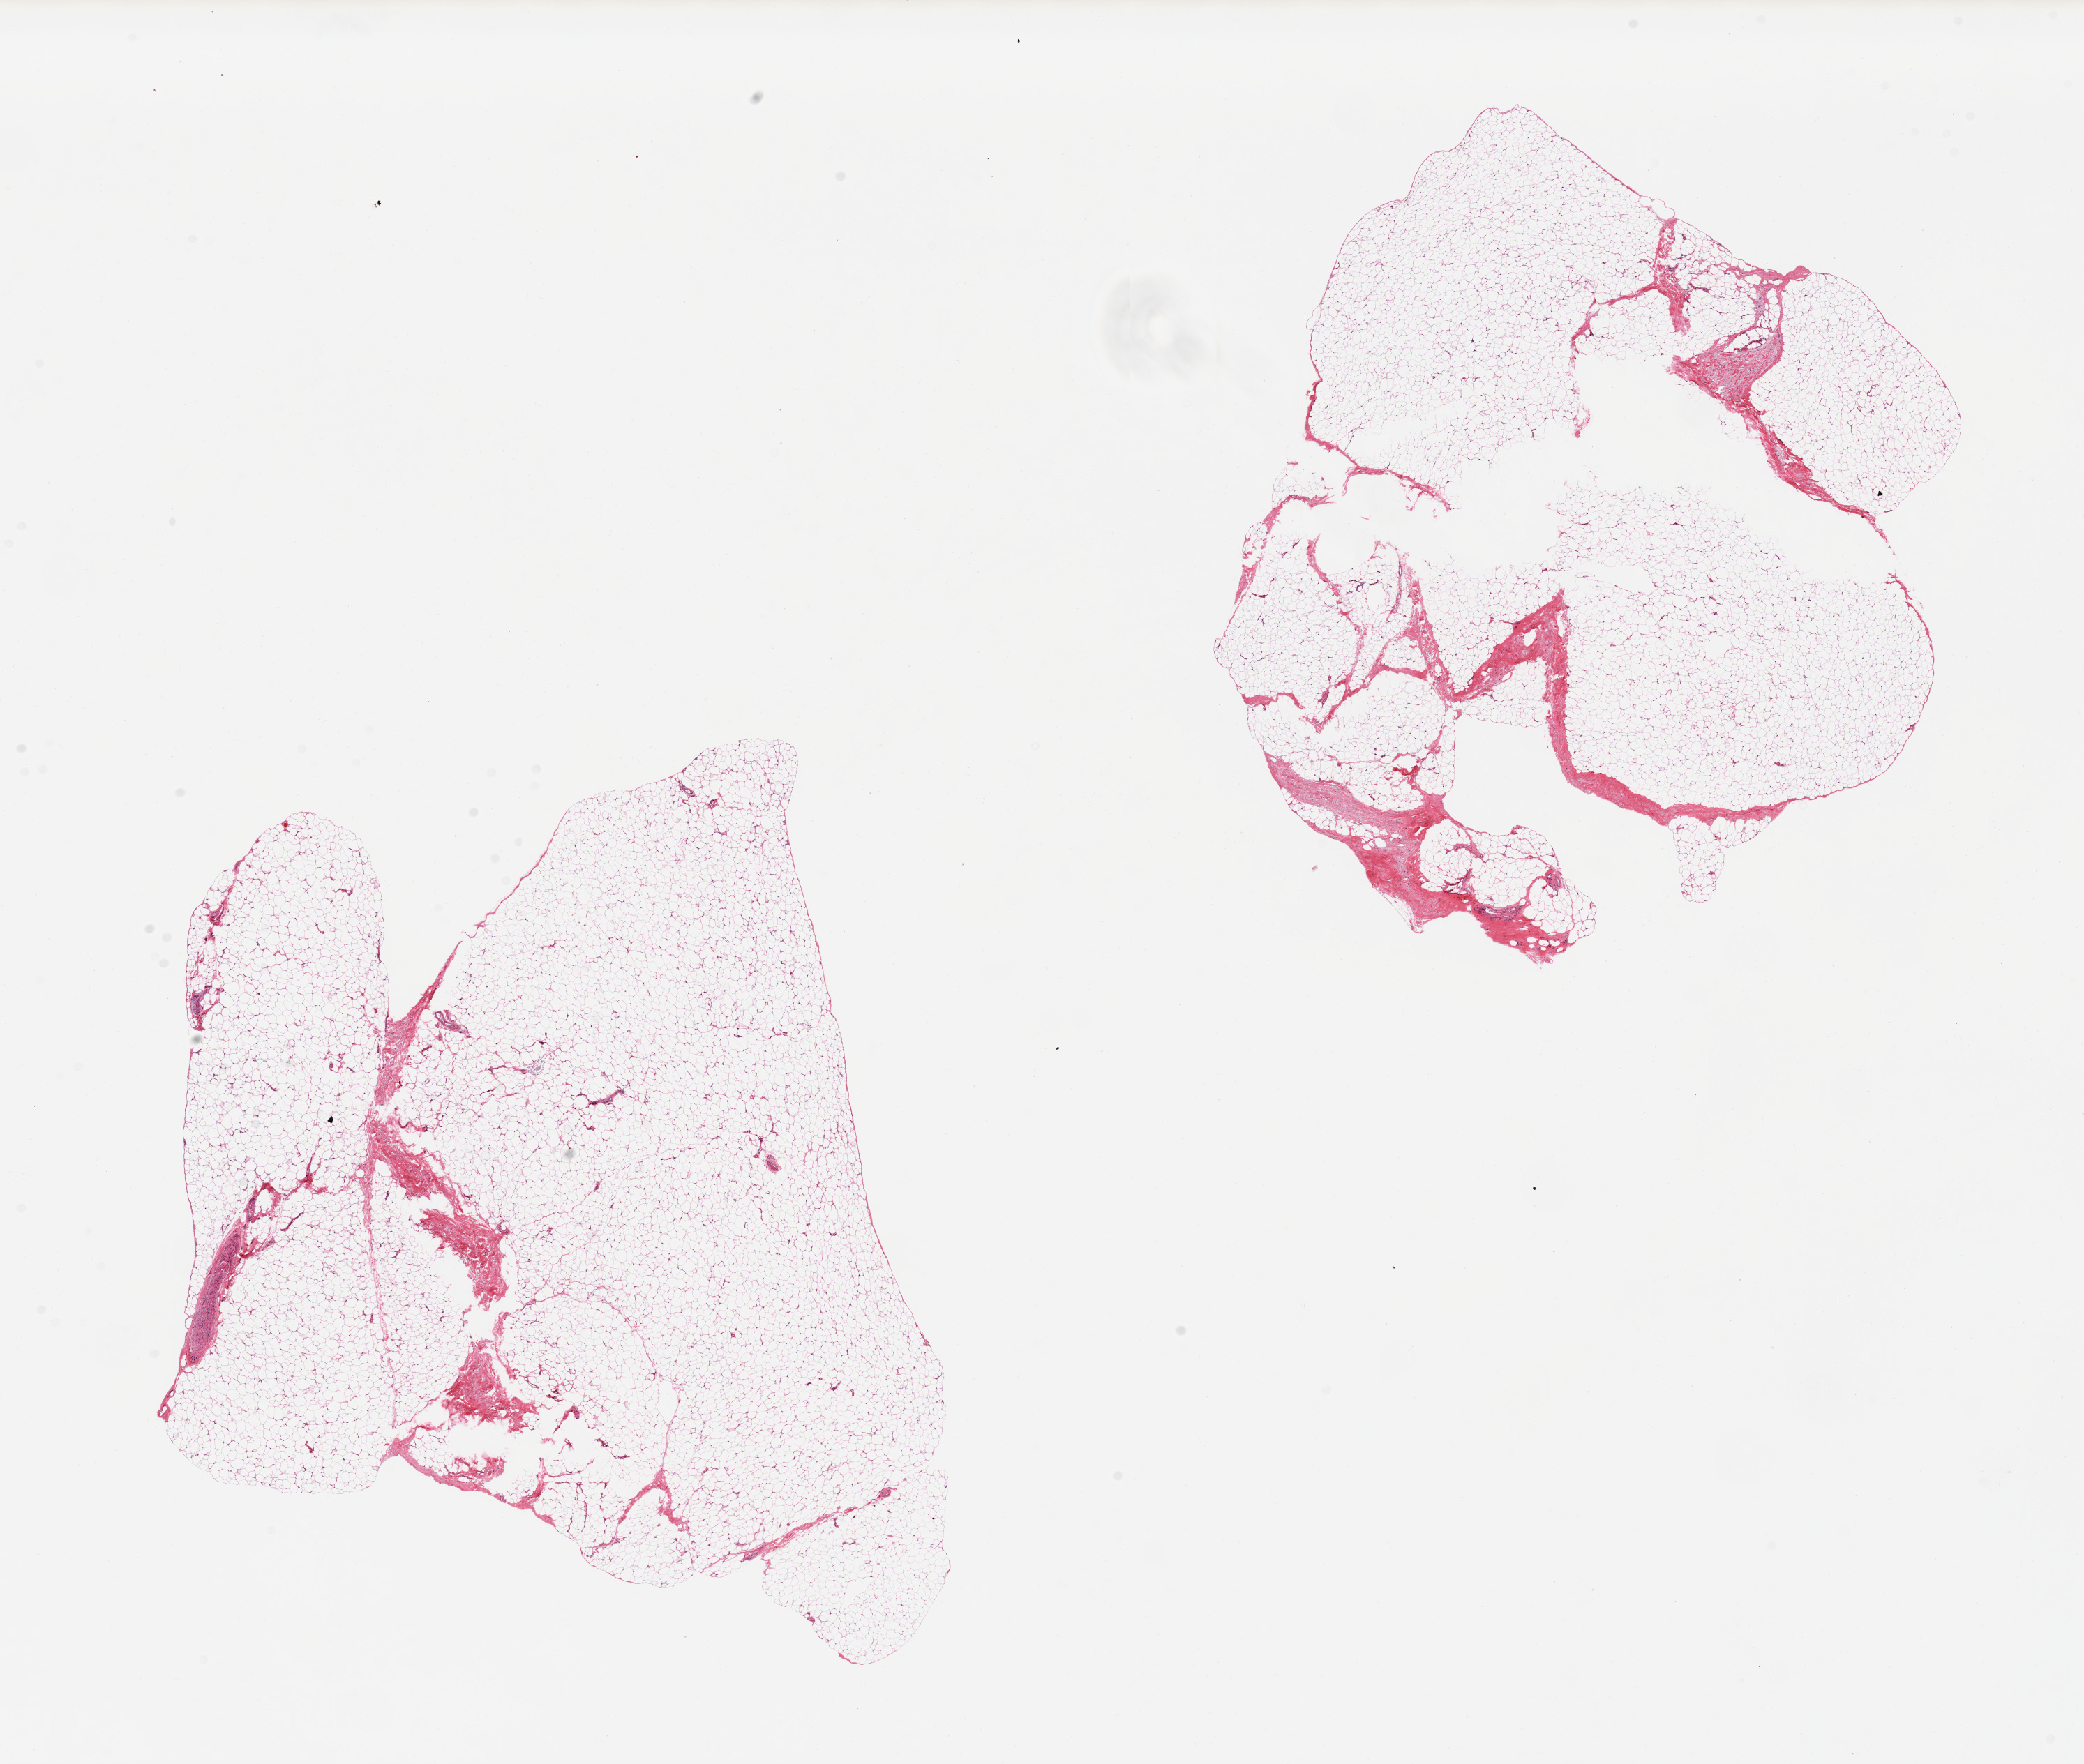
H&E whole-slide image — a low-resolution overview of the entire scanned area, about 23.6 x 20.0 mm (from a 20x scan). PAXgene-fixed, paraffin-embedded tissue. Sampled site (target tissue): adipose tissue. Donor tissue sample.
- pathologist's review note for this sample: 2 pieces, ~10-15% fibro-fascial elements